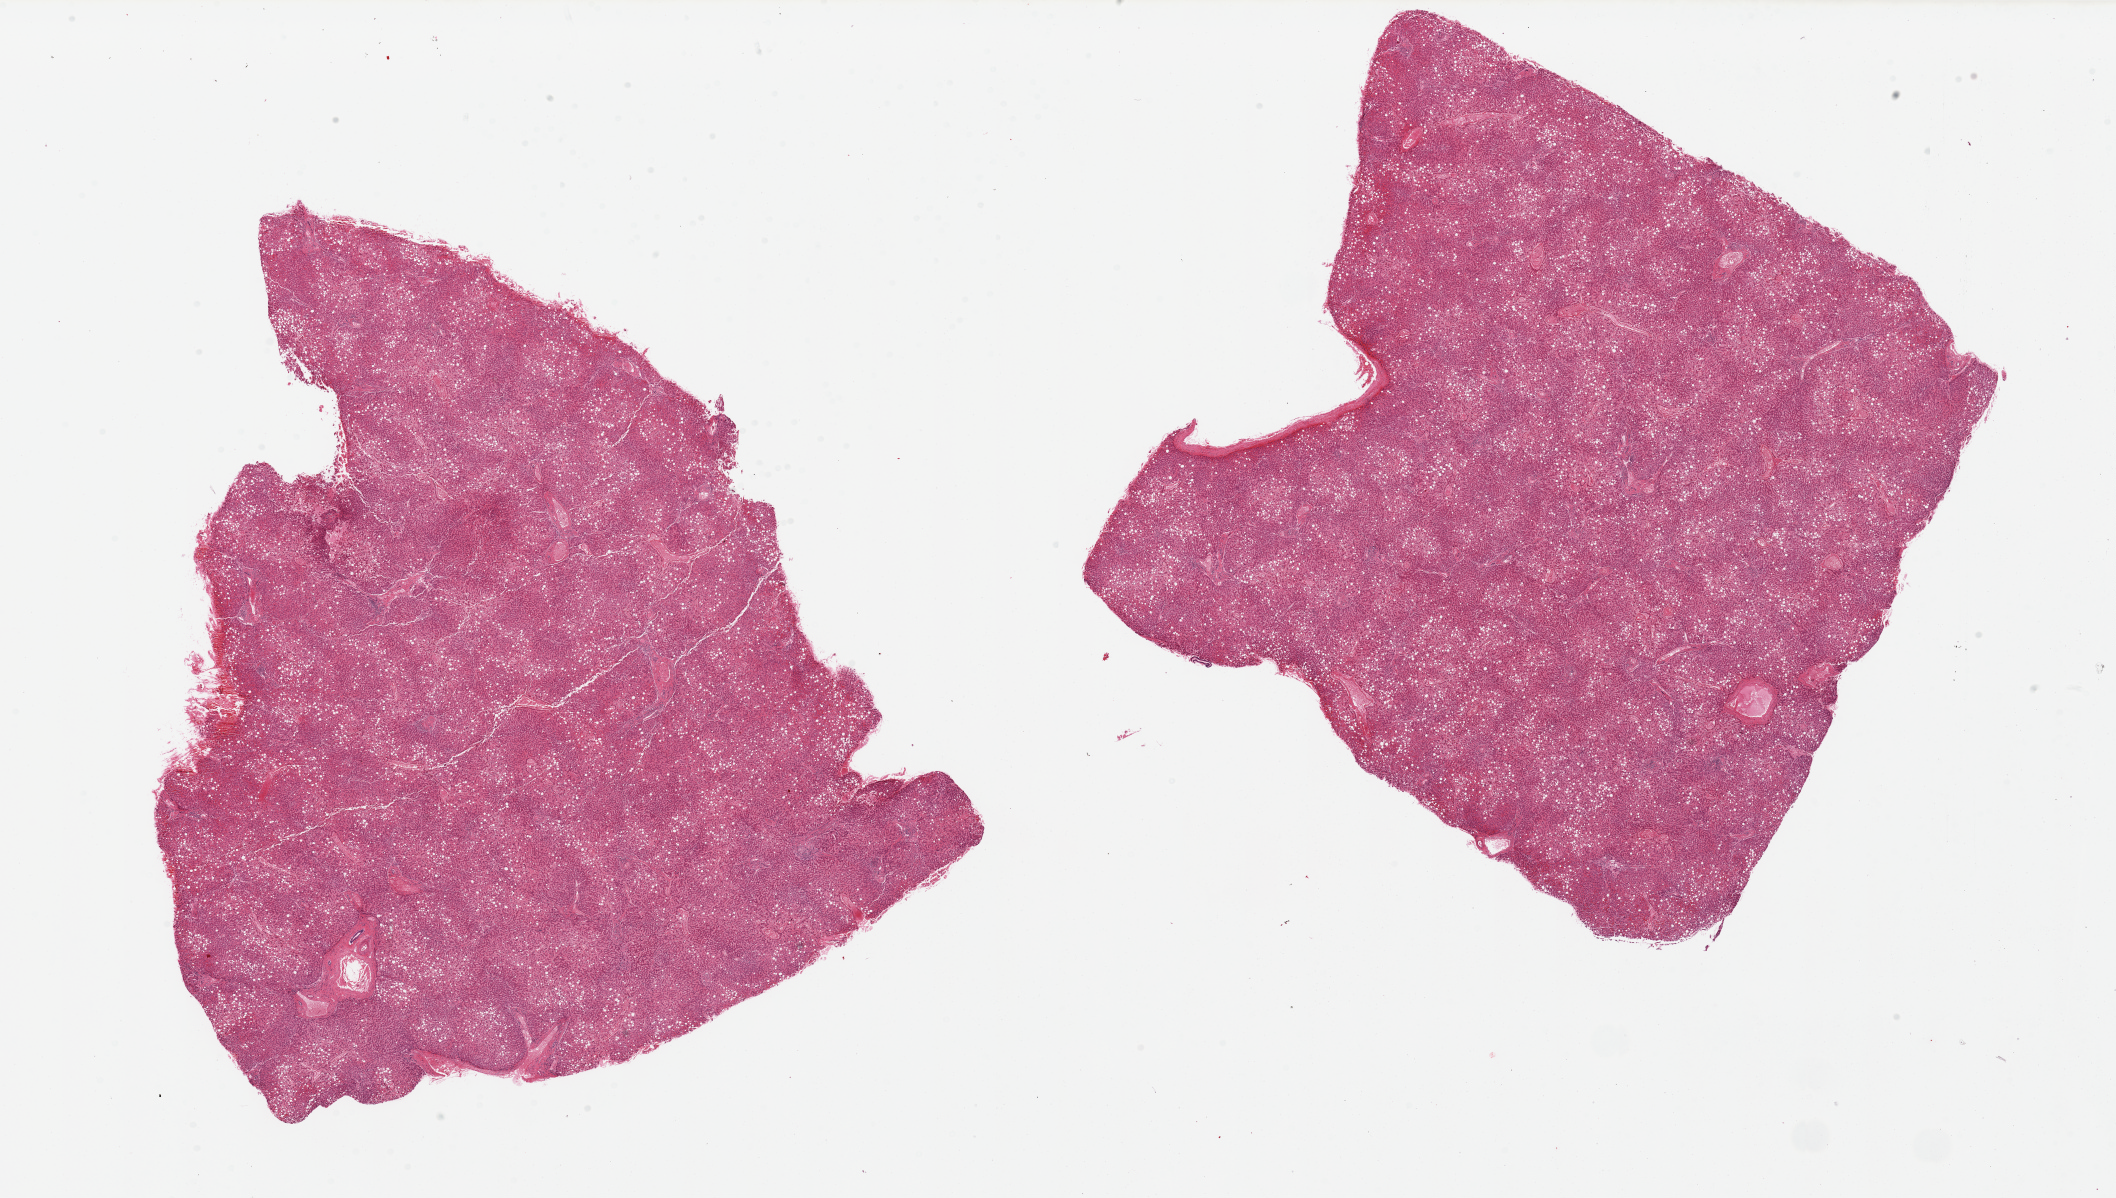
Digitized hematoxylin and eosin (H&E)-stained section — a low-resolution overview of the entire scanned area, about 33.5 x 18.9 mm, PAXgene-fixed paraffin-embedded (PFPE) section, target tissue: liver, tissue donor sample. Donor sex: male.
Review note (as recorded): 2 pieces, some congestion, diffuse macro and microvesicular steatosis.